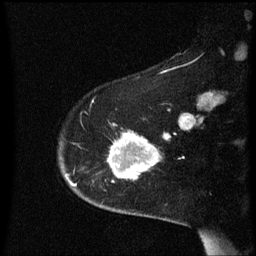
Breast MRI (dynamic contrast-enhanced), one sagittal slice; position 45 of 60 along the scan axis; dynamic contrast-enhanced series, image 2 of 3 at this slice position (ordered by acquisition); 1.5 T; TE 4.2 ms, TR 8.4 ms; 2 mm slice thickness; 256 × 256 image matrix. Female patient, age 54 years. Case-level facts recorded for this patient, not image findings: setting: breast cancer imaged before/during neoadjuvant chemotherapy; receptor status: HR-positive, HER2-negative.
Annotated regions visible in this slice (semi-automatically segmented with operator editing):
- analysis volume of interest (the breast-tissue region the enhancement analysis was run in; not a lesion): box from (x=98, y=134) to (x=172, y=183) px
- tumour enhancement mask (voxels above the 70 % enhancement threshold inside the analysis volume of interest): (x=109, y=134)–(x=171, y=179)